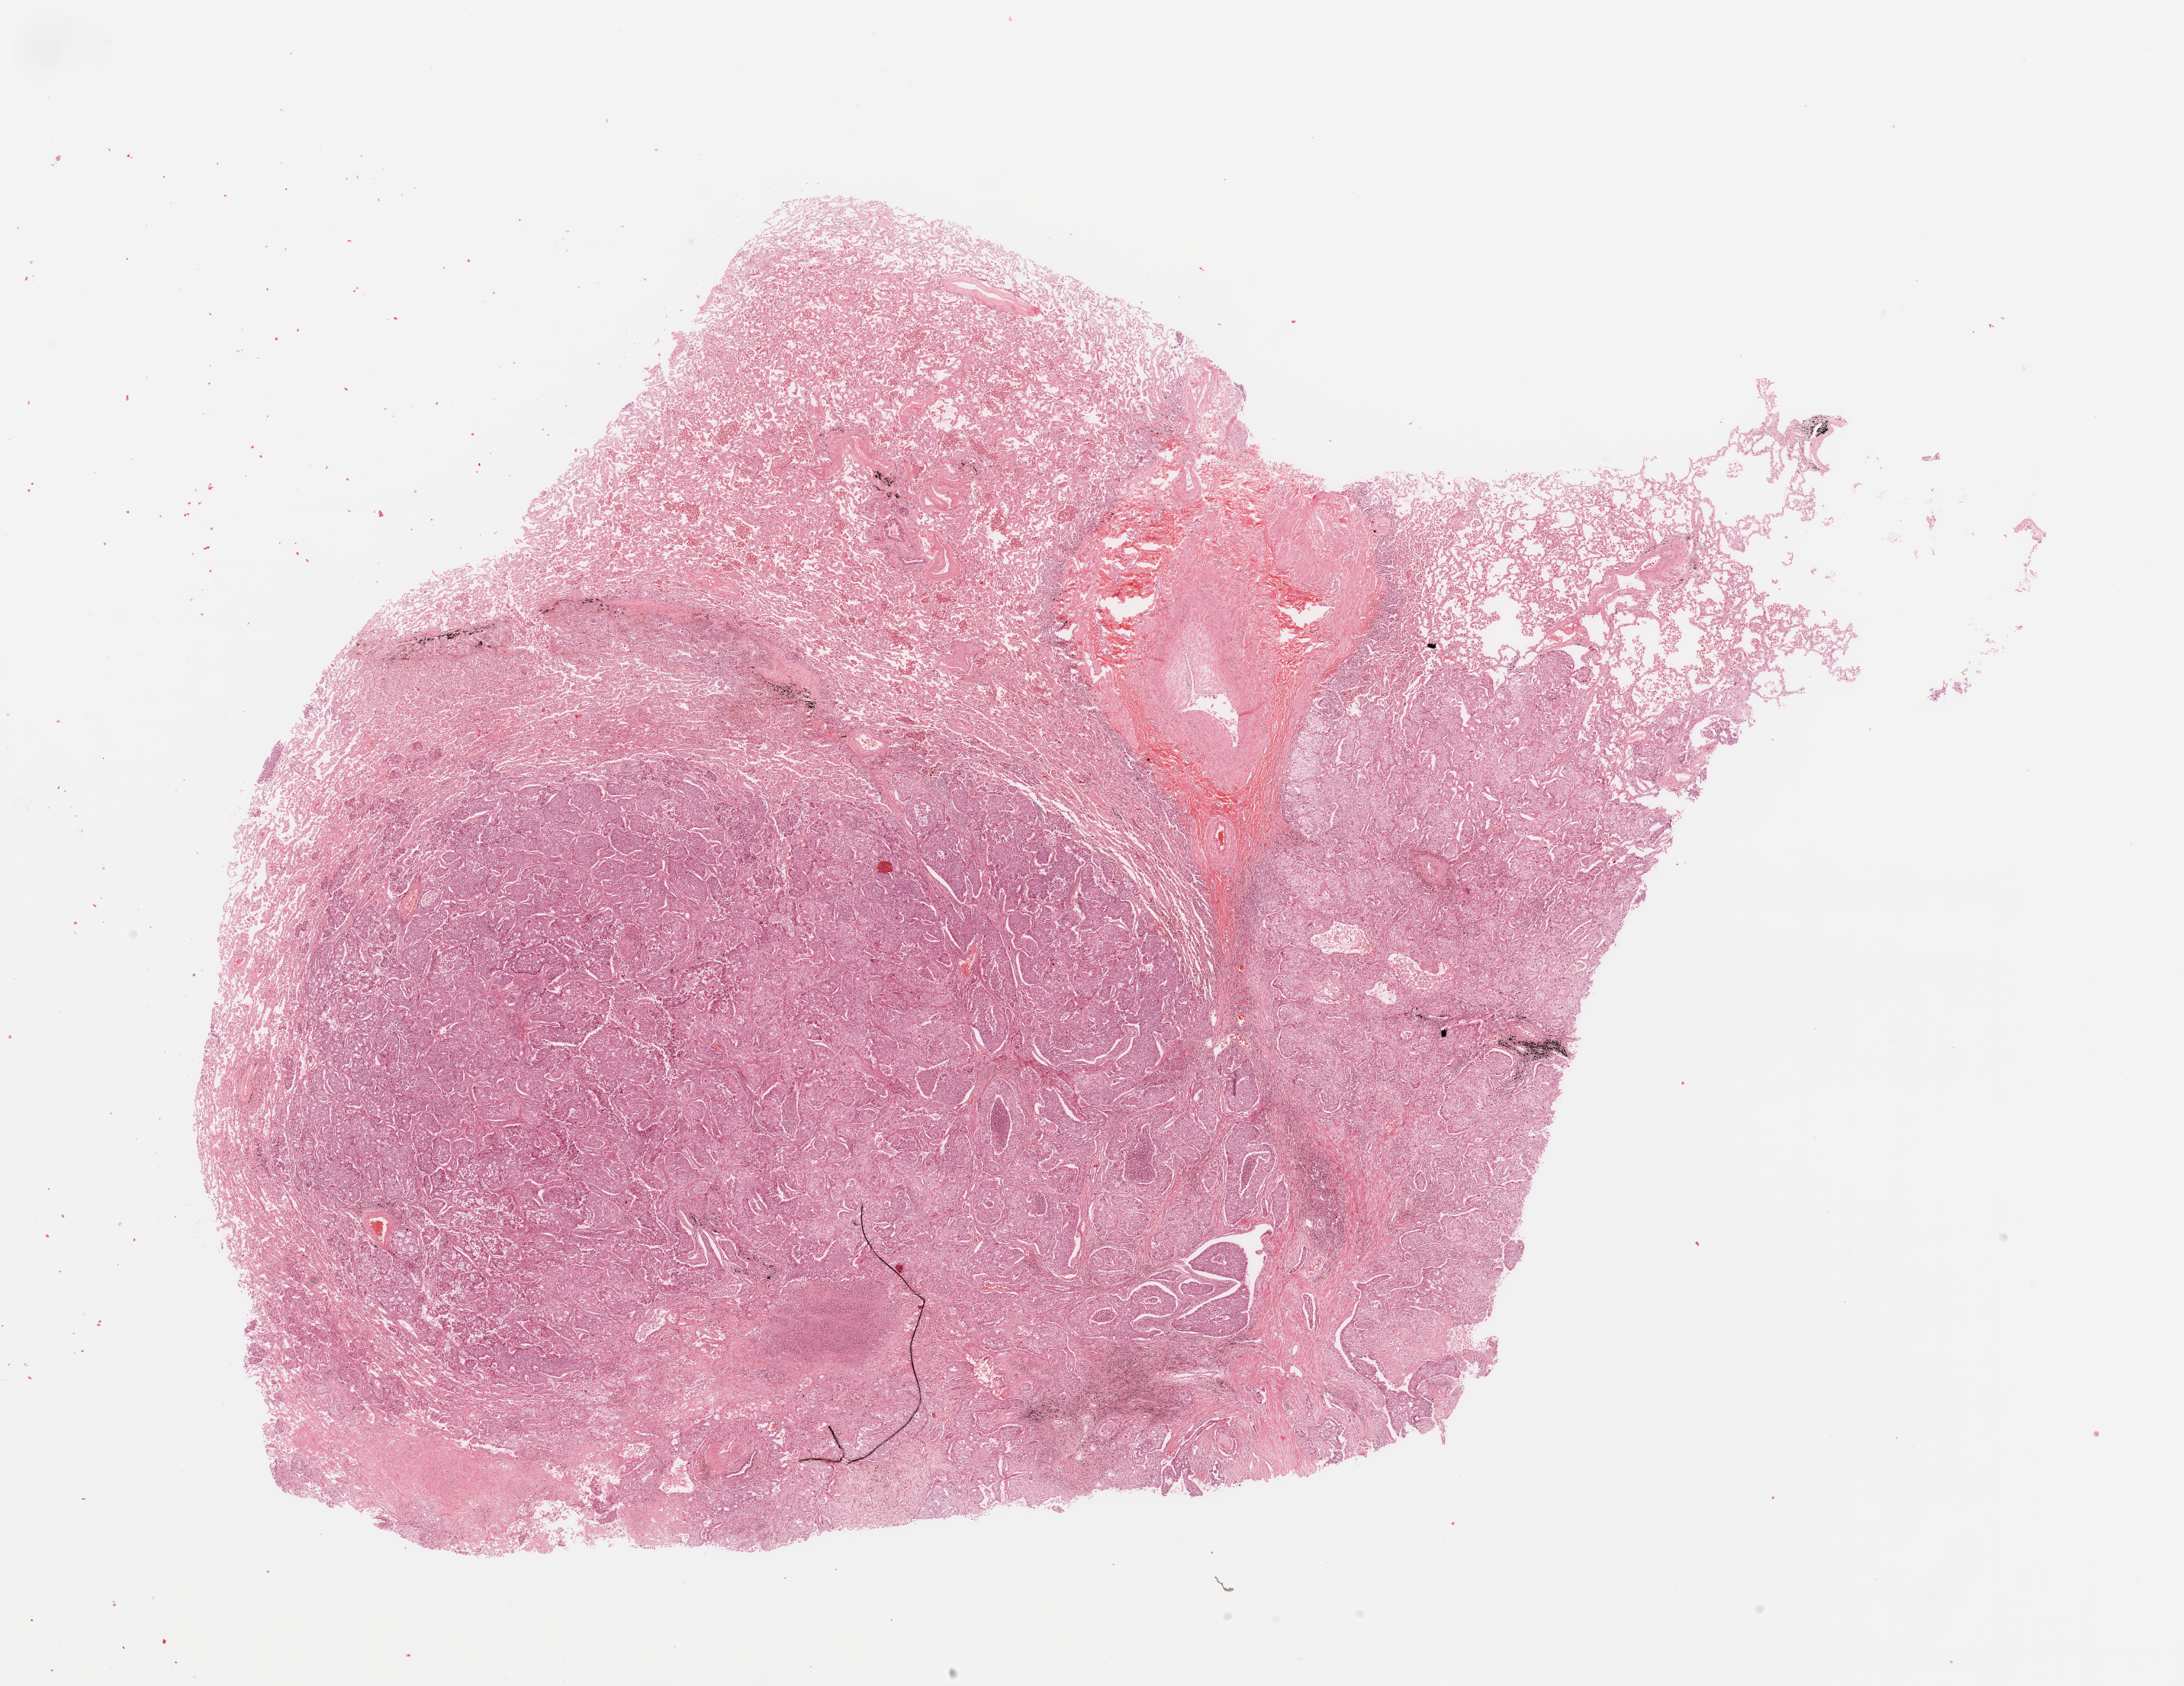
Whole-slide histology image, H&E-stained — whole scanned area (about 22.6 x 17.5 mm) shown as a low-resolution overview; tumour tissue sample, lung. Patient: male, age 57 years. Histologic grade: G2 (moderately differentiated).
• histologic diagnosis: Adenocarcinoma, NOS
• AJCC pathologic stage: IB